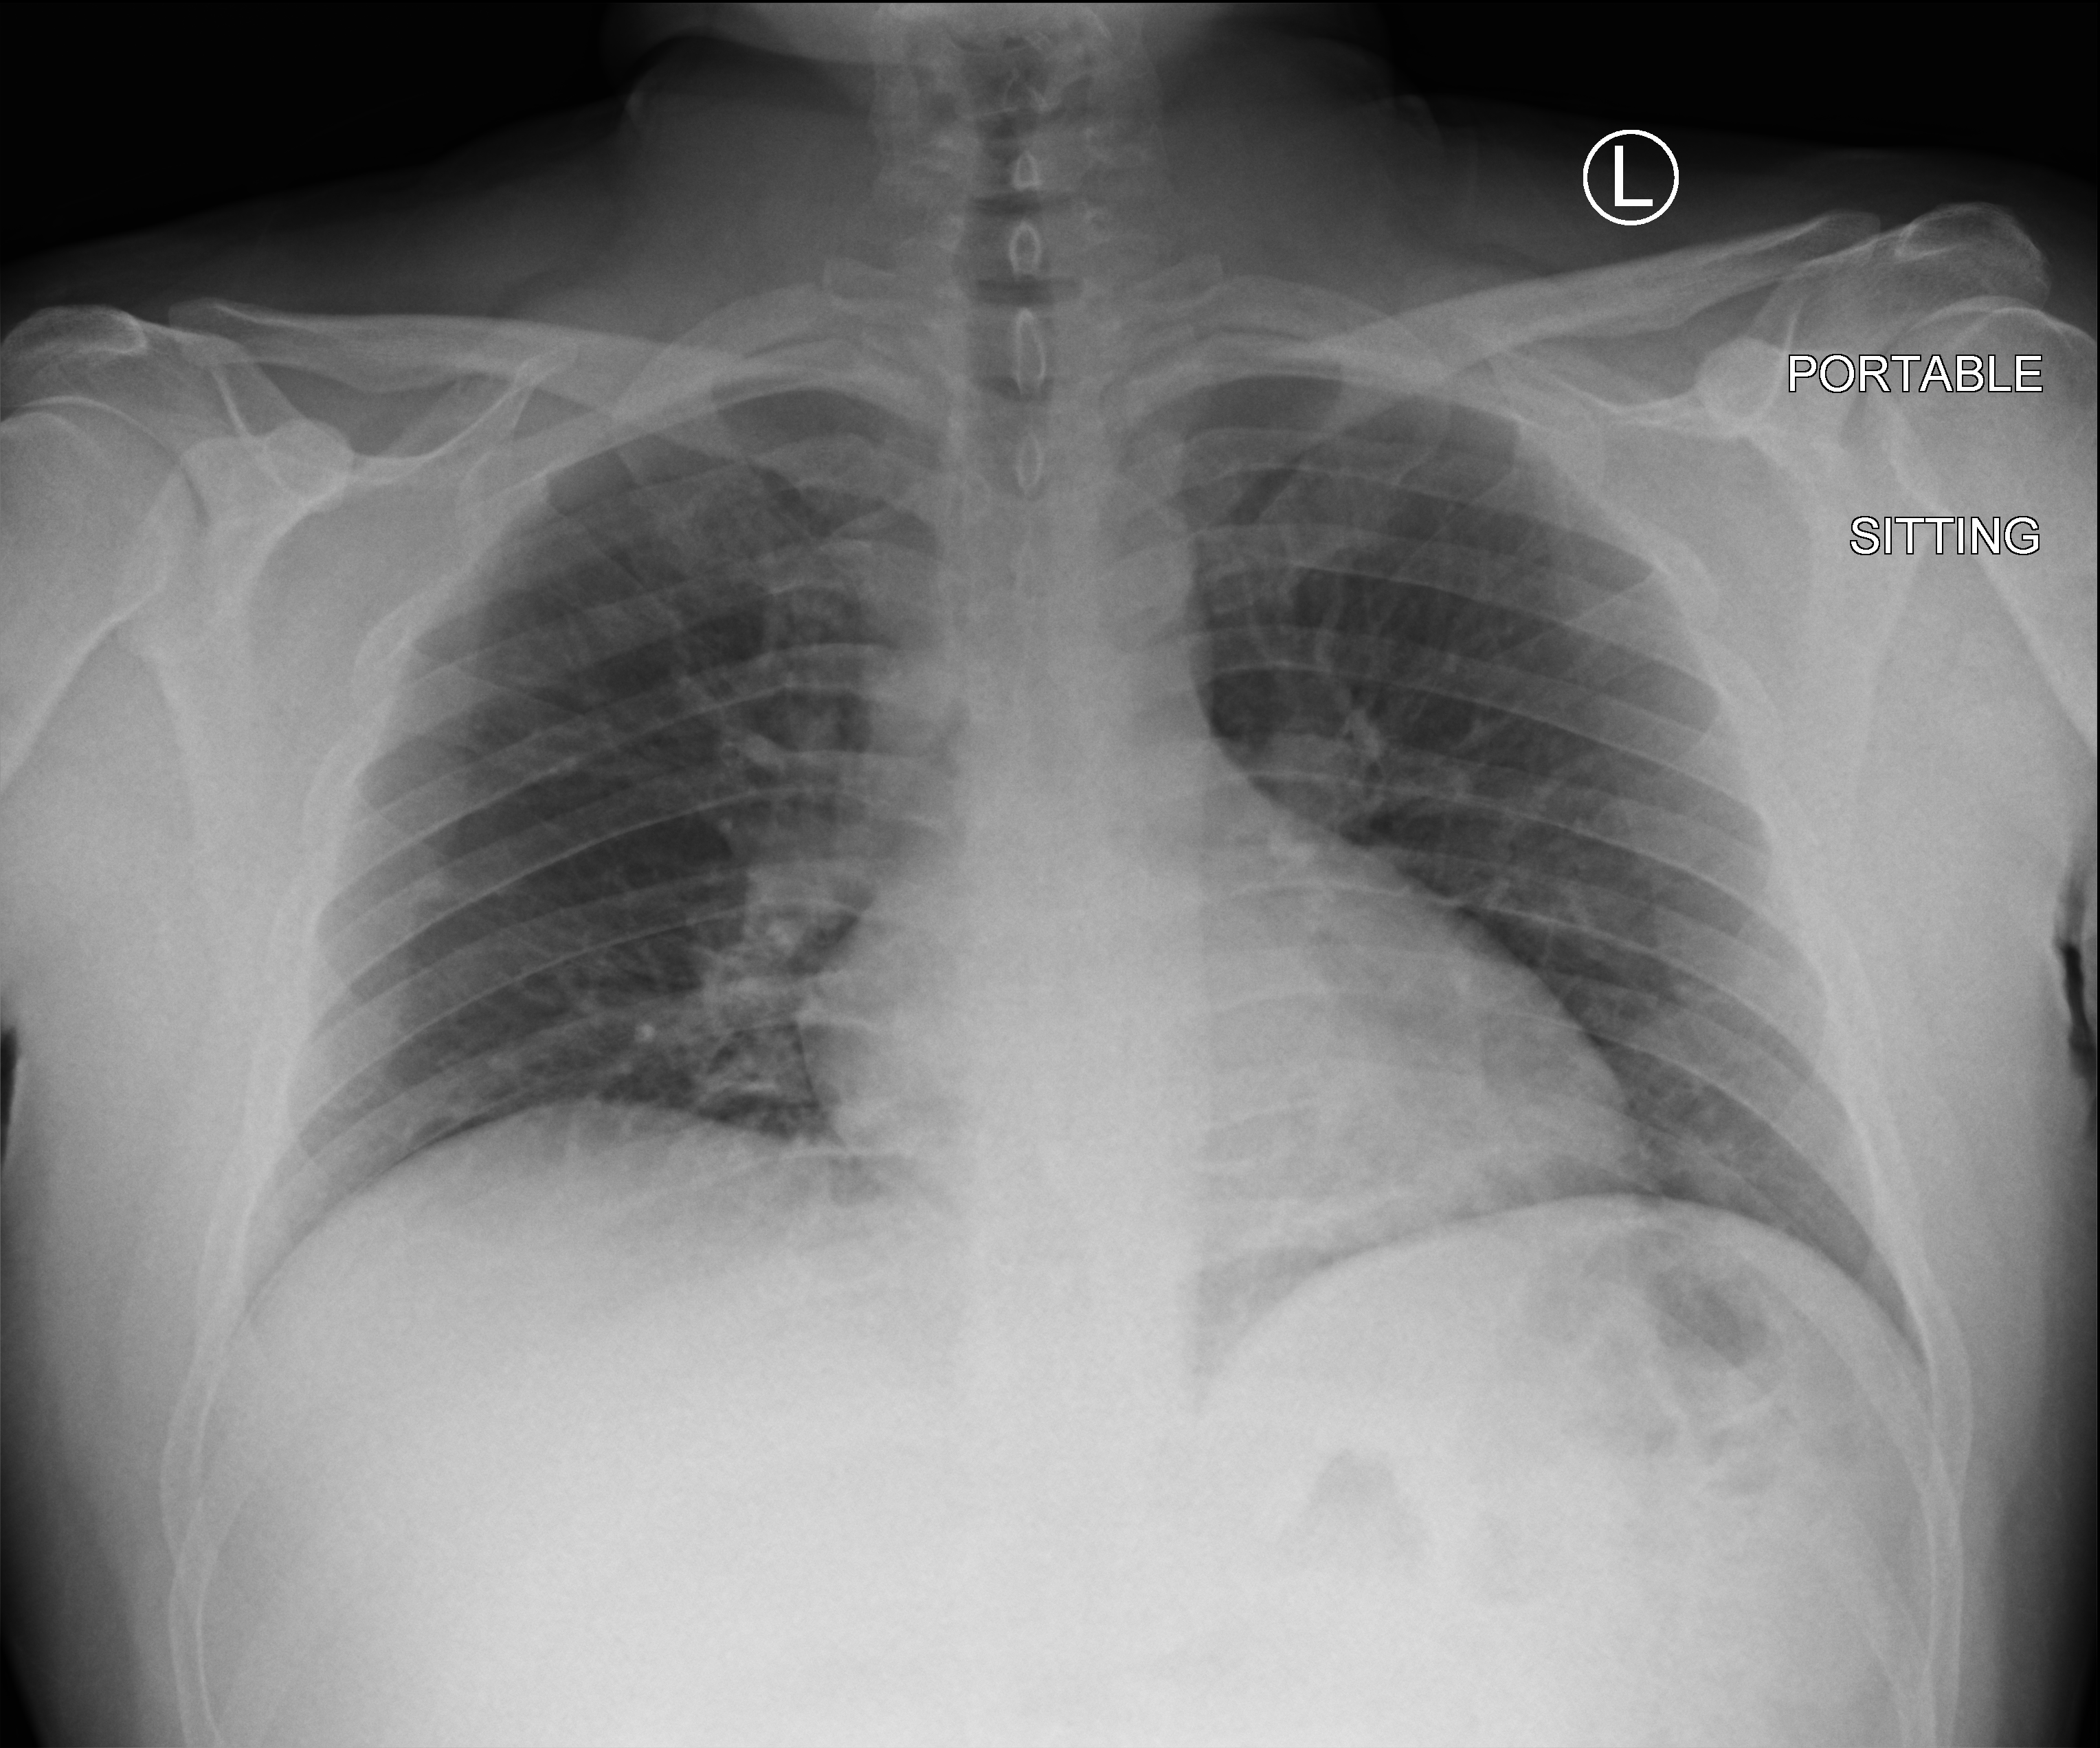
Bedside chest radiograph (computed radiography), anteroposterior (AP) projection. Patient hospitalised with COVID-19; male, aged 18–59 years.
Admission-level facts for this patient (not findings on this image; timing relative to this image not recorded):
- COPD (admission record): no
- admitted to intensive care during this hospital stay: no